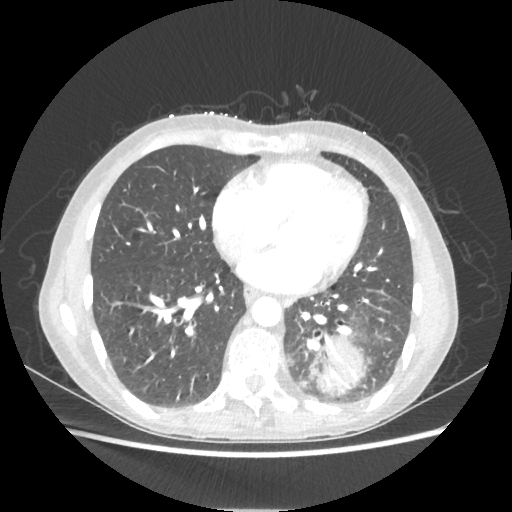
Chest CT, one axial slice. Slice 84 of 221 in the series (ordered by position). Reconstruction kernel STANDARD. 80 kVp. Lung window (W 1500 / L -600 HU). 1.25 mm slice thickness. 512 × 512 image matrix, field of view 360 × 360 mm. Patient: female, 53 years. Case-level facts recorded for this patient, not image findings: clinical TNM (as recorded): T3 N0 M0.
Annotated regions visible in this slice (bounding box drawn by a radiologist):
- lung tumour (recorded histology: adenocarcinoma): bounding box <313,332,364,396> (left, top, right, bottom; pixels)